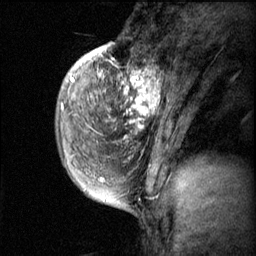
Breast MRI (dynamic contrast-enhanced), one sagittal slice; position 15 of 60 along the scan axis; dynamic contrast-enhanced series, image 2 of 3 at this slice position (ordered by acquisition); 1.5 T; TE 4.2 ms, TR 11.1 ms; 256 × 256 image matrix, field of view 180 × 180 mm. Patient: female, 50 years.
Outlined on this slice (semi-automatically segmented with operator editing):
- analysis volume of interest (the breast-tissue region the enhancement analysis was run in; not a lesion): box from (x=82, y=56) to (x=168, y=143) px
- tumour enhancement mask (voxels above the 70 % enhancement threshold inside the analysis volume of interest): (x=82, y=56)–(x=161, y=131)